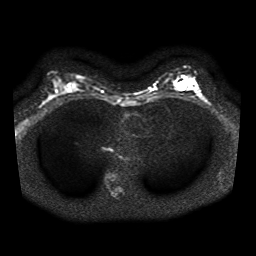
Breast MRI, one axial slice; slice 22 of 41 in the series (ordered by position); diffusion-weighted series; image 2 of 4 stored at this slice position (different b-values; order by instance number); 1.5 T; 5 mm slice thickness; 256 × 256 image matrix, field of view 320 × 320 mm. Female patient.
Annotated regions visible in this slice (outlined manually by an expert reader):
- tumour on diffusion-weighted imaging: bounding box [x1, y1, x2, y2] px = [187, 79, 196, 89]